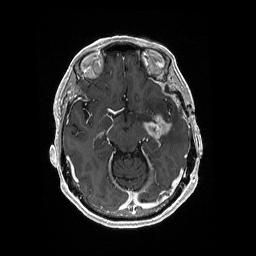
Brain MRI from a brain-tumour surgery series, one axial slice; position 112 of 176 along the scan axis; T1-weighted post-contrast; 1 mm slice thickness; 256 × 256 image matrix, field of view 256 × 256 mm. Case-level facts recorded for this patient, not image findings: histopathology: Glioblastoma; WHO grade: 4; IDH mutation: no.
Structures marked on this image (manually delineated by an expert):
- tumour: bounding box <143,114,173,139> (left, top, right, bottom; pixels)